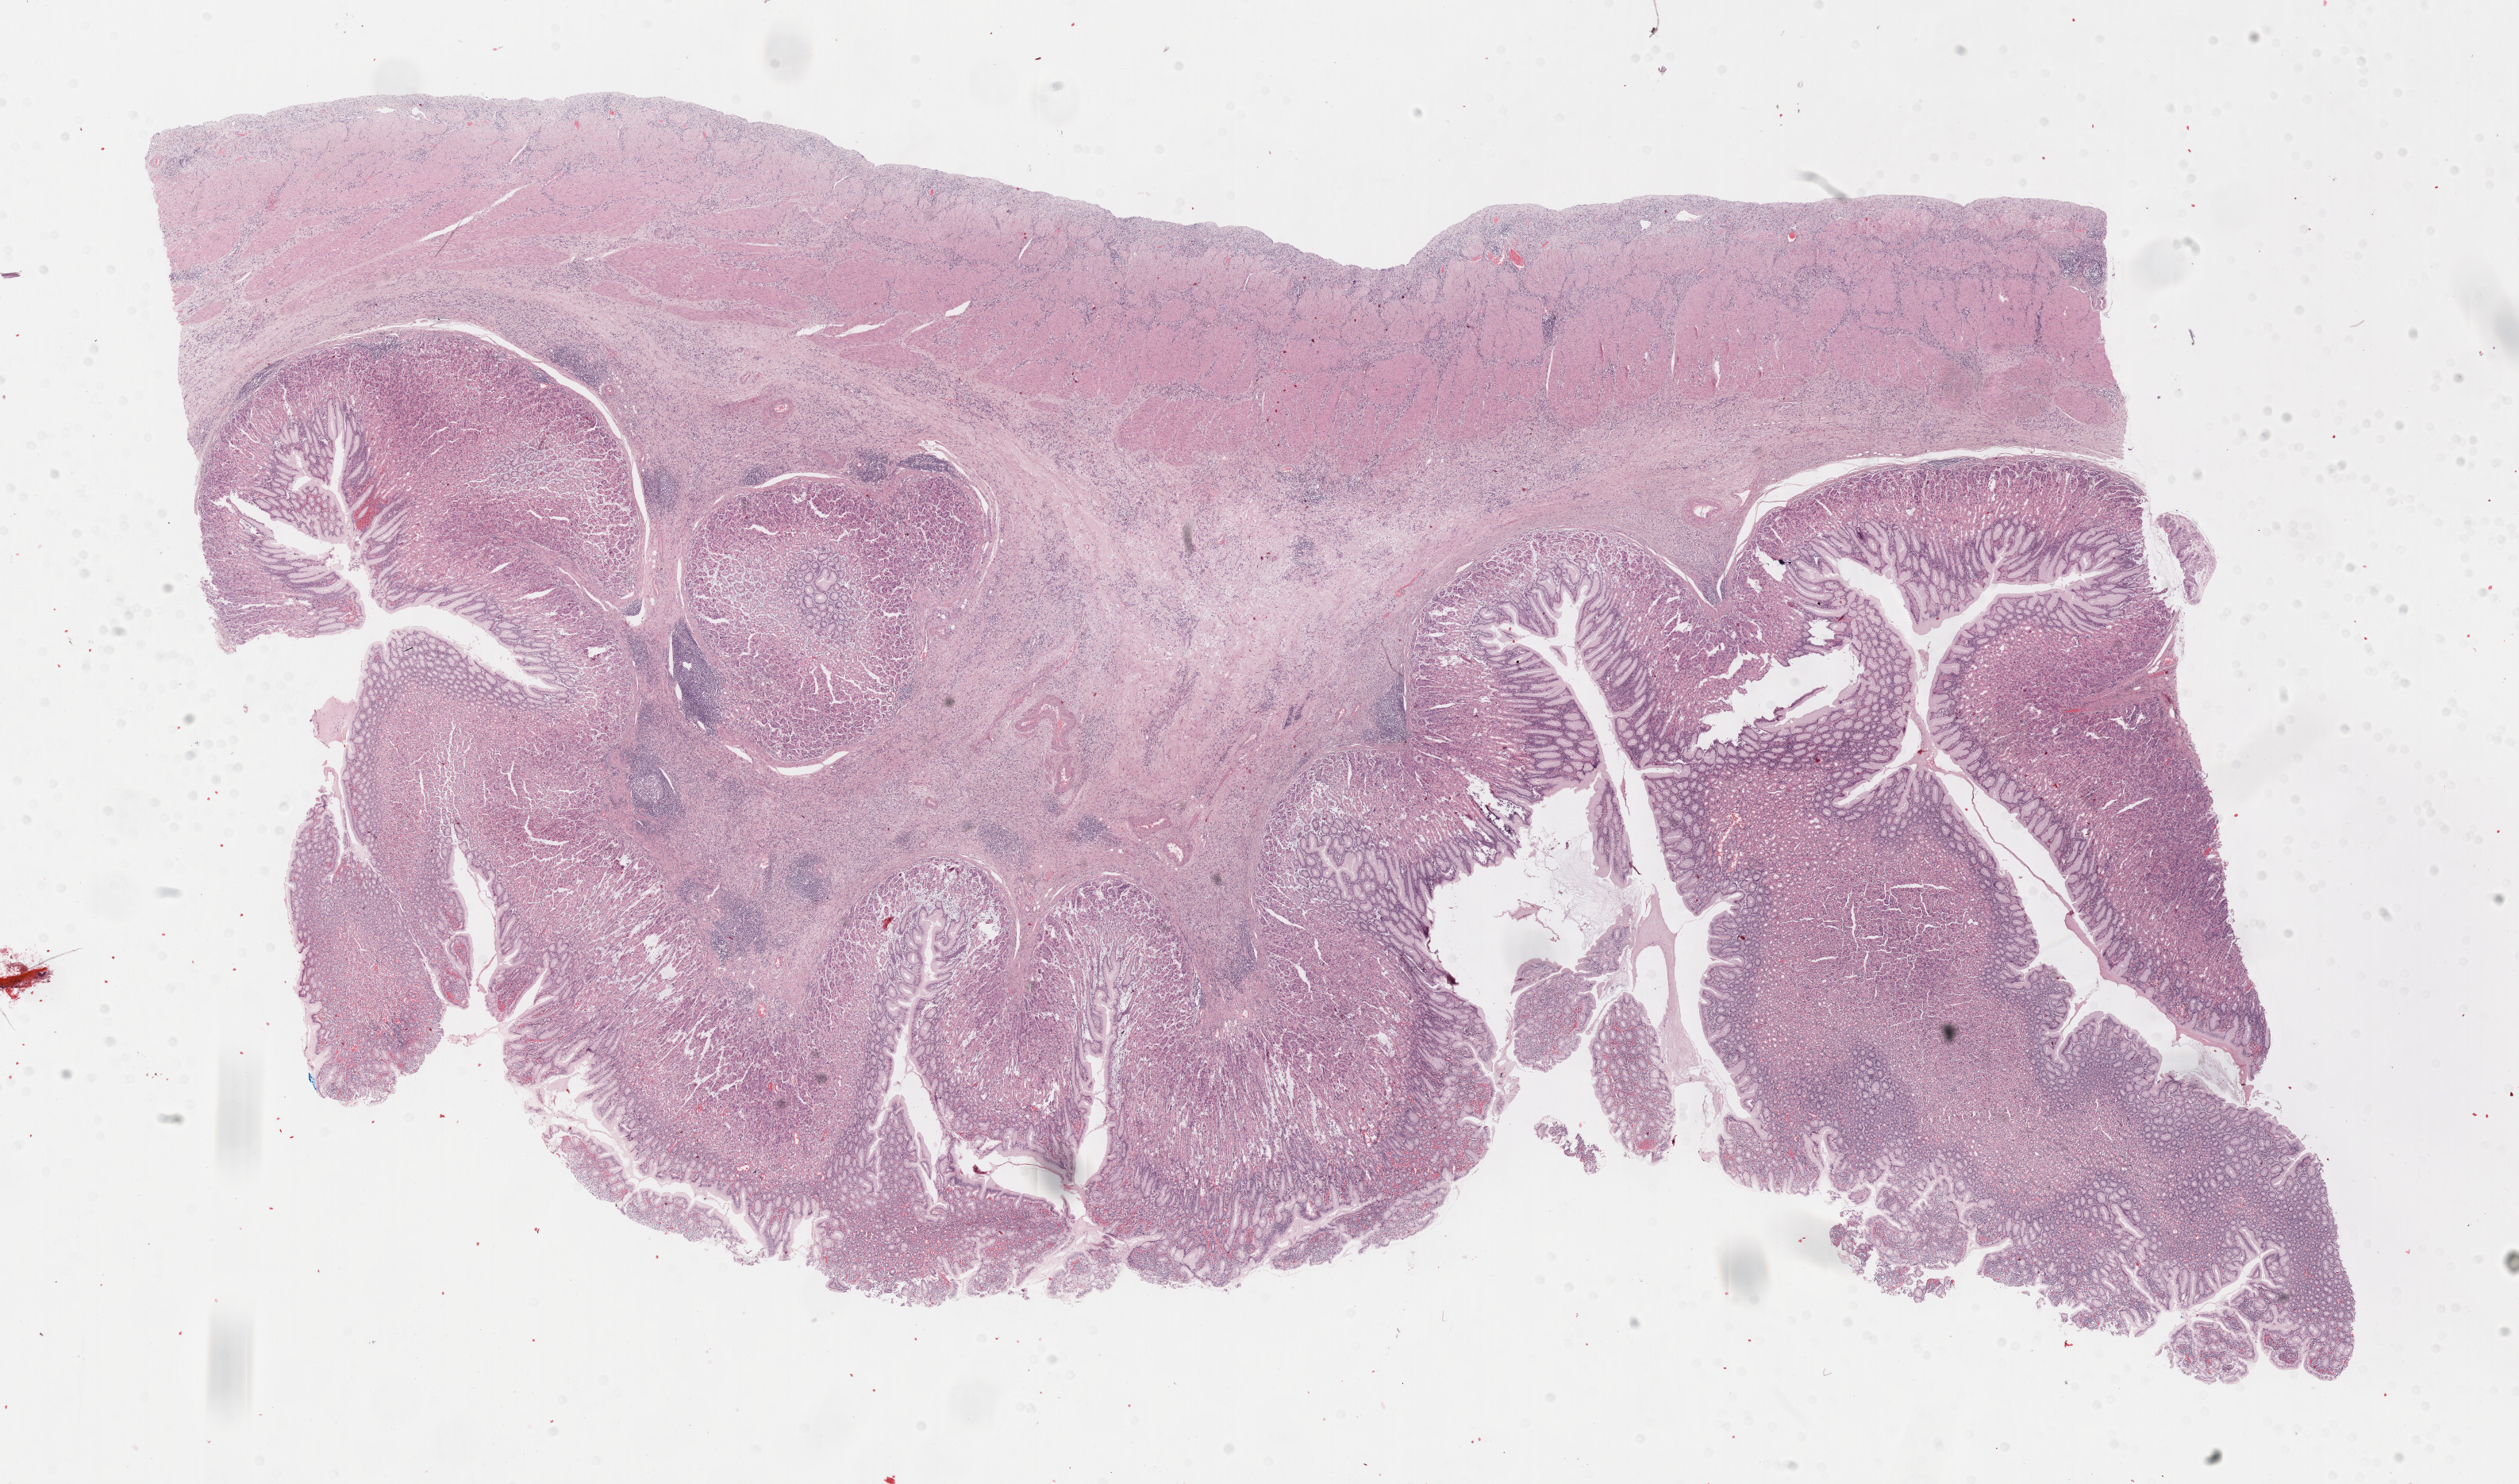
Whole-slide histology image, H&E, whole scanned area (about 25.7 x 15.1 mm, from a 40x scan) shown as a low-resolution overview, formalin-fixed paraffin-embedded (FFPE) diagnostic section, stomach, primary tumour sample. Patient: female, age at initial diagnosis 52 years. Histologic grade: G3 (poorly differentiated).
AJCC pathologic stage: IIIB (7th edition). Diagnosis: Carcinoma, diffuse type (fundus of stomach). Lymph nodes positive (case pathology): 13 of 22 examined.